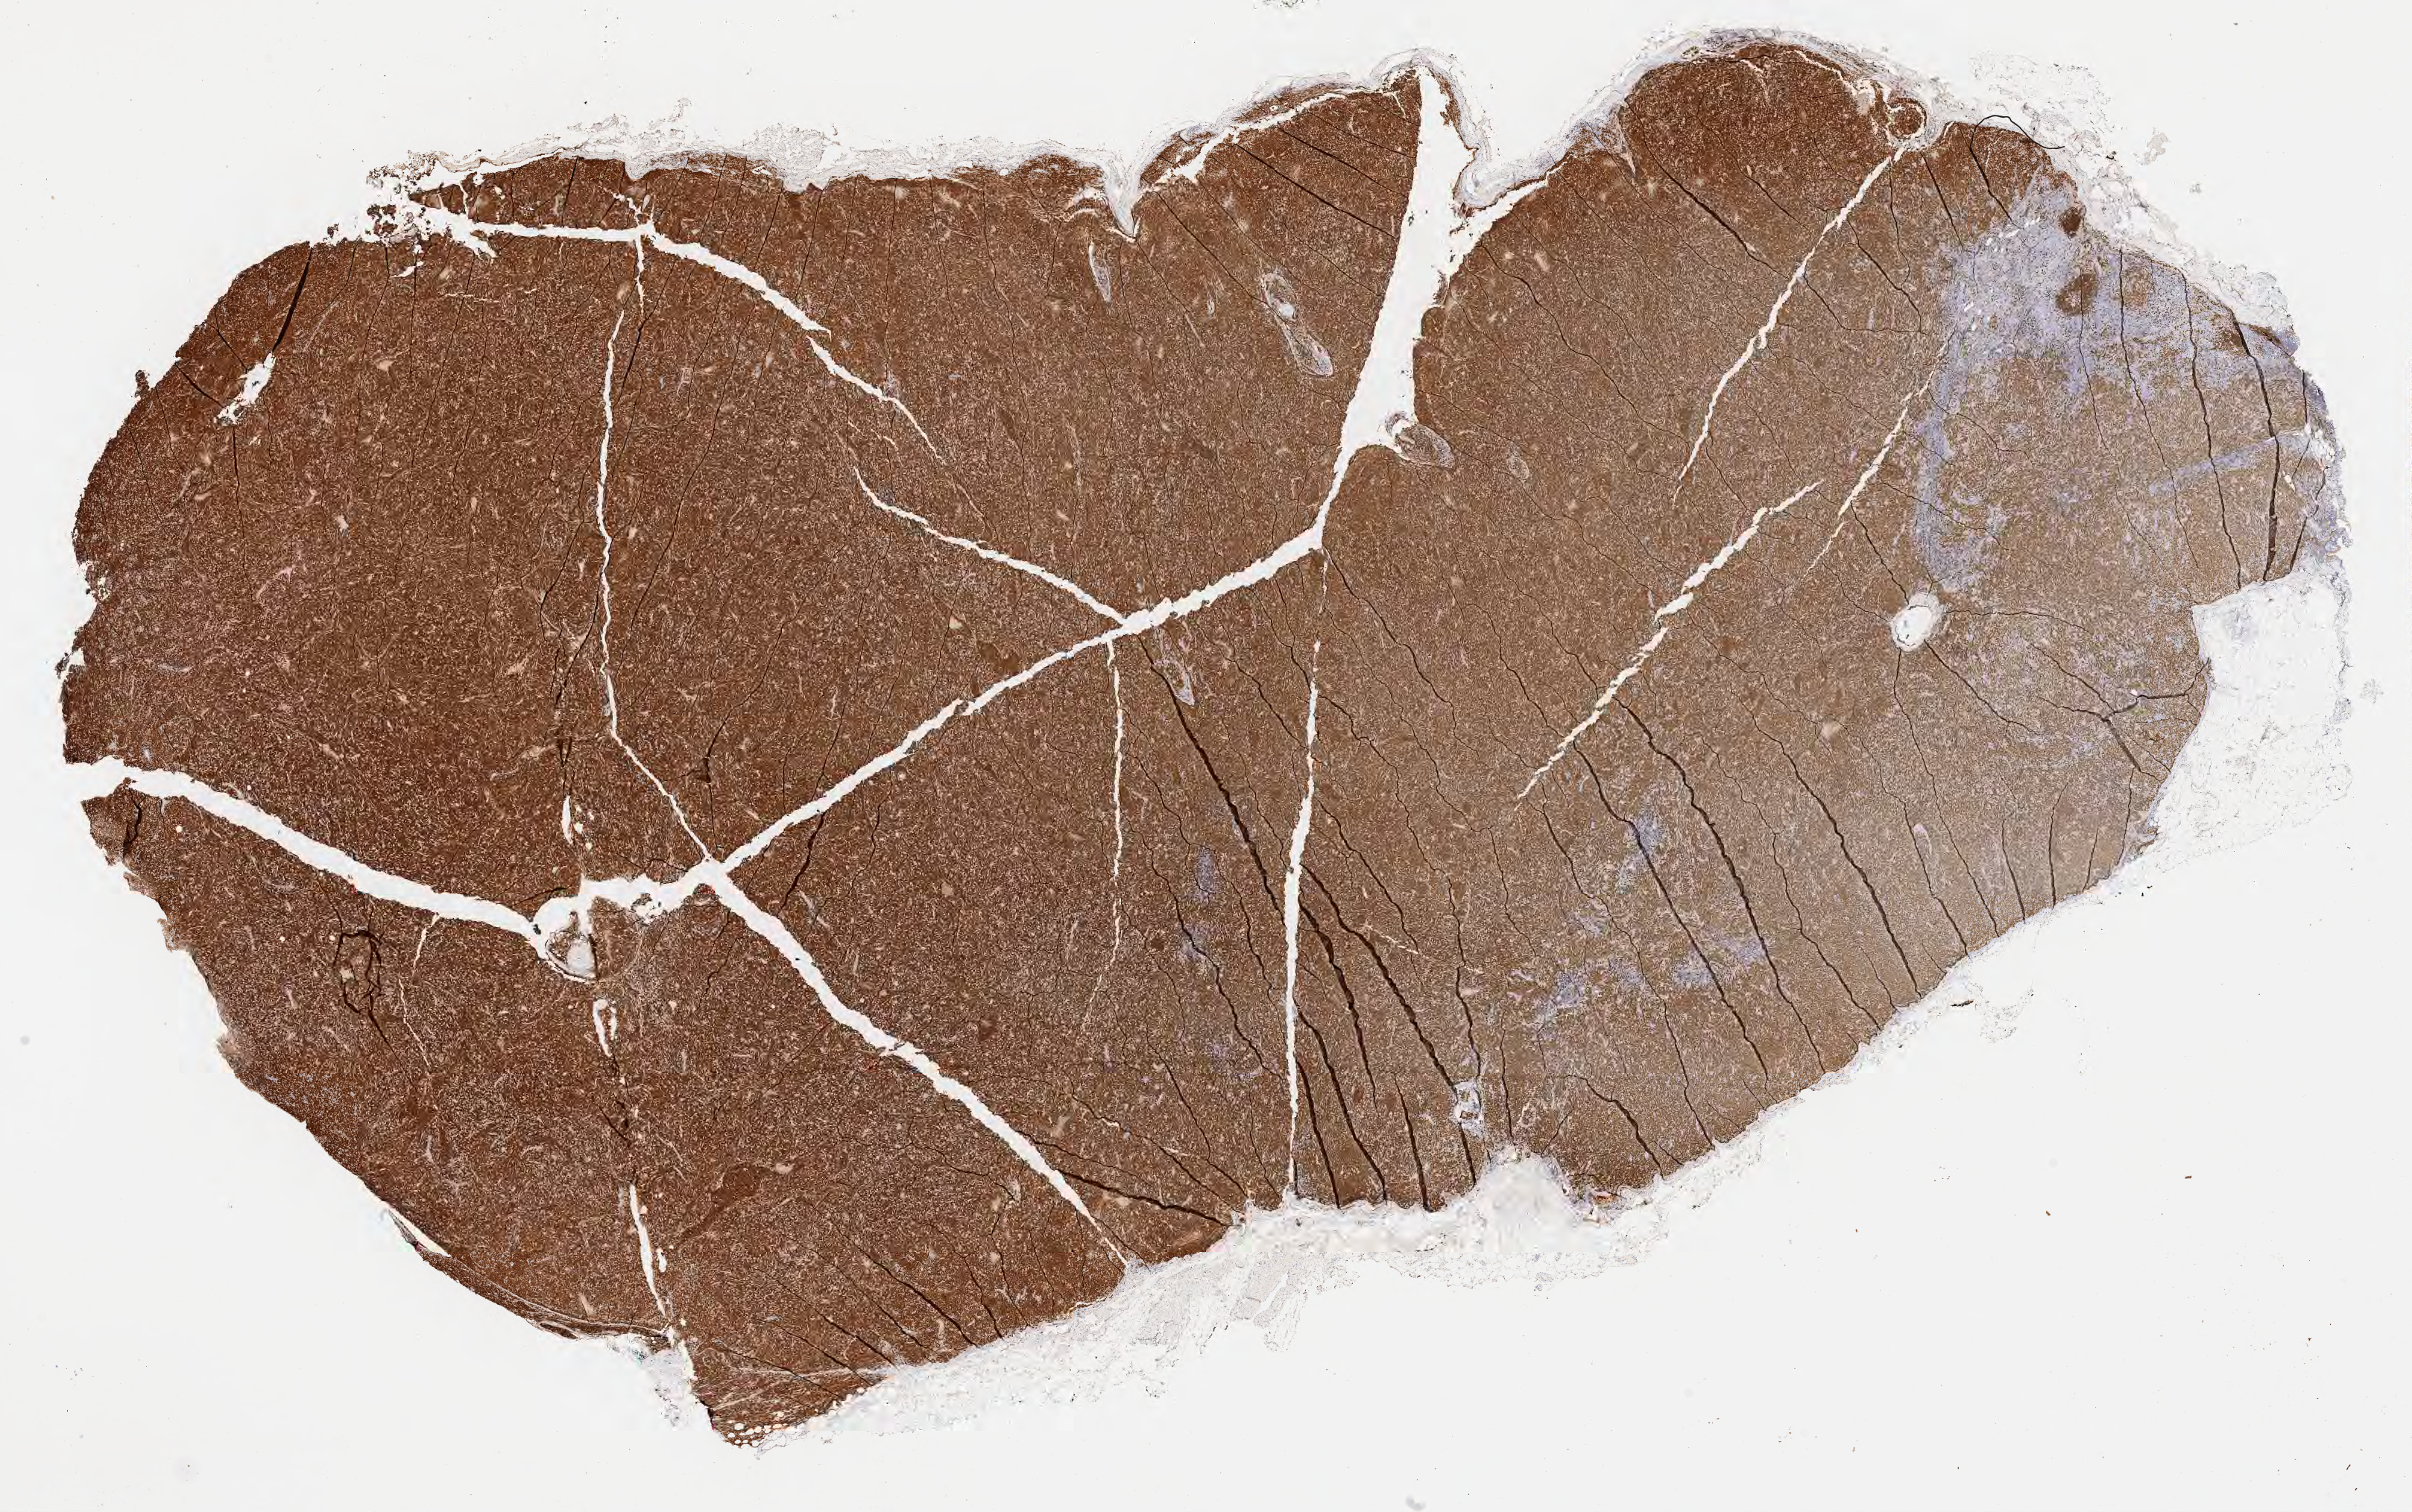
Whole-slide image, immunohistochemical stain for CD79a, a low-resolution overview of the entire scanned area, about 26.2 x 16.4 mm, tumor tissue. Male patient, 69 years old.
Diagnosis: Diffuse large B-cell lymphoma, NOS.